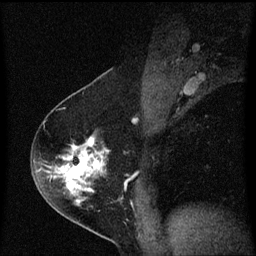
Breast MRI (dynamic contrast-enhanced), one sagittal slice; position 38 of 60 along the scan axis; dynamic contrast-enhanced series, image 2 of 3 at this slice position (ordered by acquisition); 1.5 T; TE 4.2 ms, TR 8.4 ms; 2 mm slice thickness; 256 × 256 image matrix, field of view 200 × 200 mm. Female patient, age 54 years. From the clinical record (not read from this slice): setting: breast cancer imaged before/during neoadjuvant chemotherapy; receptor status: HER2-positive.
Annotated regions visible in this slice (semi-automatic segmentation, software-assisted and operator-edited):
- analysis volume of interest (the breast-tissue region the enhancement analysis was run in; not a lesion): box from (x=32, y=122) to (x=109, y=213) px
- tumour enhancement mask (voxels above the 70 % enhancement threshold inside the analysis volume of interest): (x=48, y=138)–(x=103, y=193)